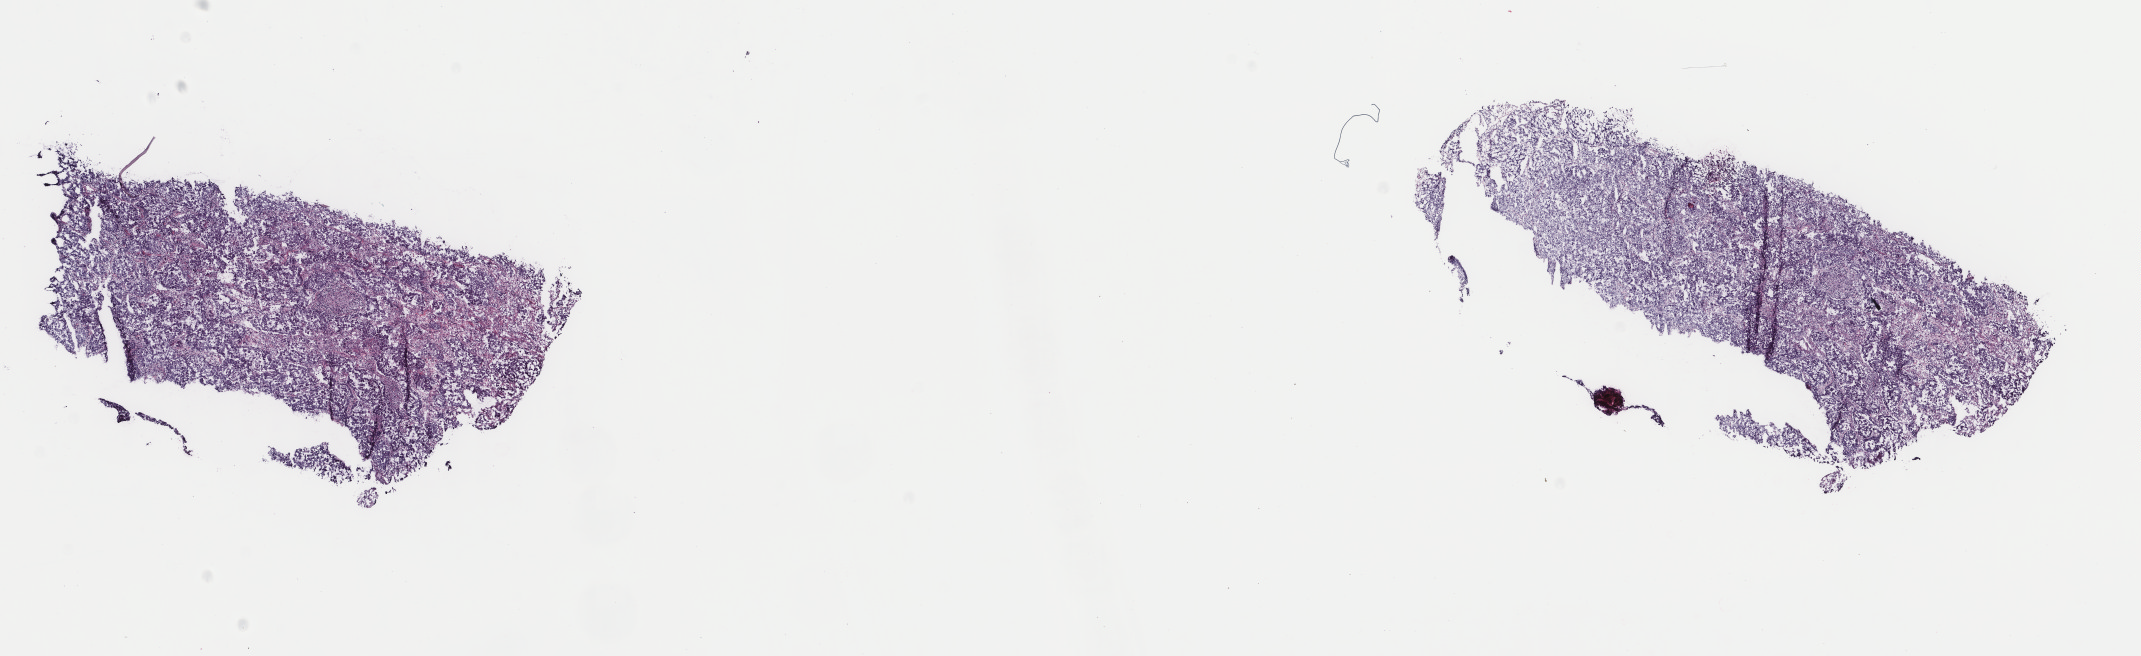
Whole-slide histology image, H&E-stained — whole scanned area (about 17.0 x 5.2 mm) shown as a low-resolution overview, frozen section, lung, primary tumour sample. Female patient; age at initial diagnosis 78 years. Slide review estimates, as recorded: tumour cells 100%, tumour nuclei 78%, normal cells 0%, stromal cells 0%, necrosis 0%. Inflammatory infiltration, as recorded: lymphocyte infiltration 0%, monocyte infiltration 0%, neutrophil infiltration 0%.
Pathologic diagnosis: Adenocarcinoma, NOS (upper lobe, lung). AJCC pathologic stage: IB (7th edition). Laterality: right.